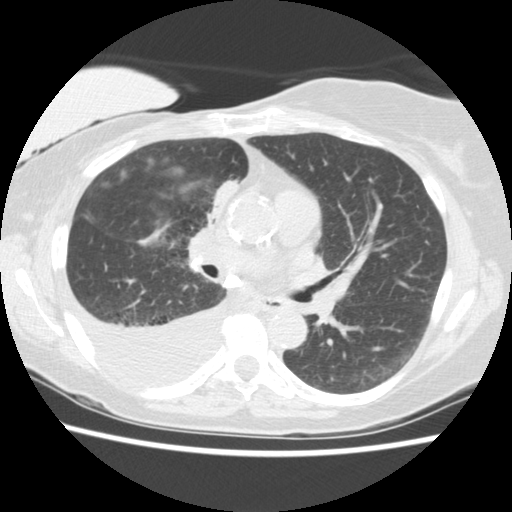
Low-dose screening chest CT, one axial slice. Slice 84 of 157 in the series (ordered by position). Reconstruction kernel STANDARD. 120 kVp. Lung window (W 1500 / L -600 HU). 2.5 mm slice thickness. 512 × 512 image matrix, field of view 330 × 330 mm.
Annotated regions visible in this slice (expert manual segmentation):
- lesion 1 (tumor, upper lobe of right lung): bounding box [x1, y1, x2, y2] px = [212, 180, 240, 219]